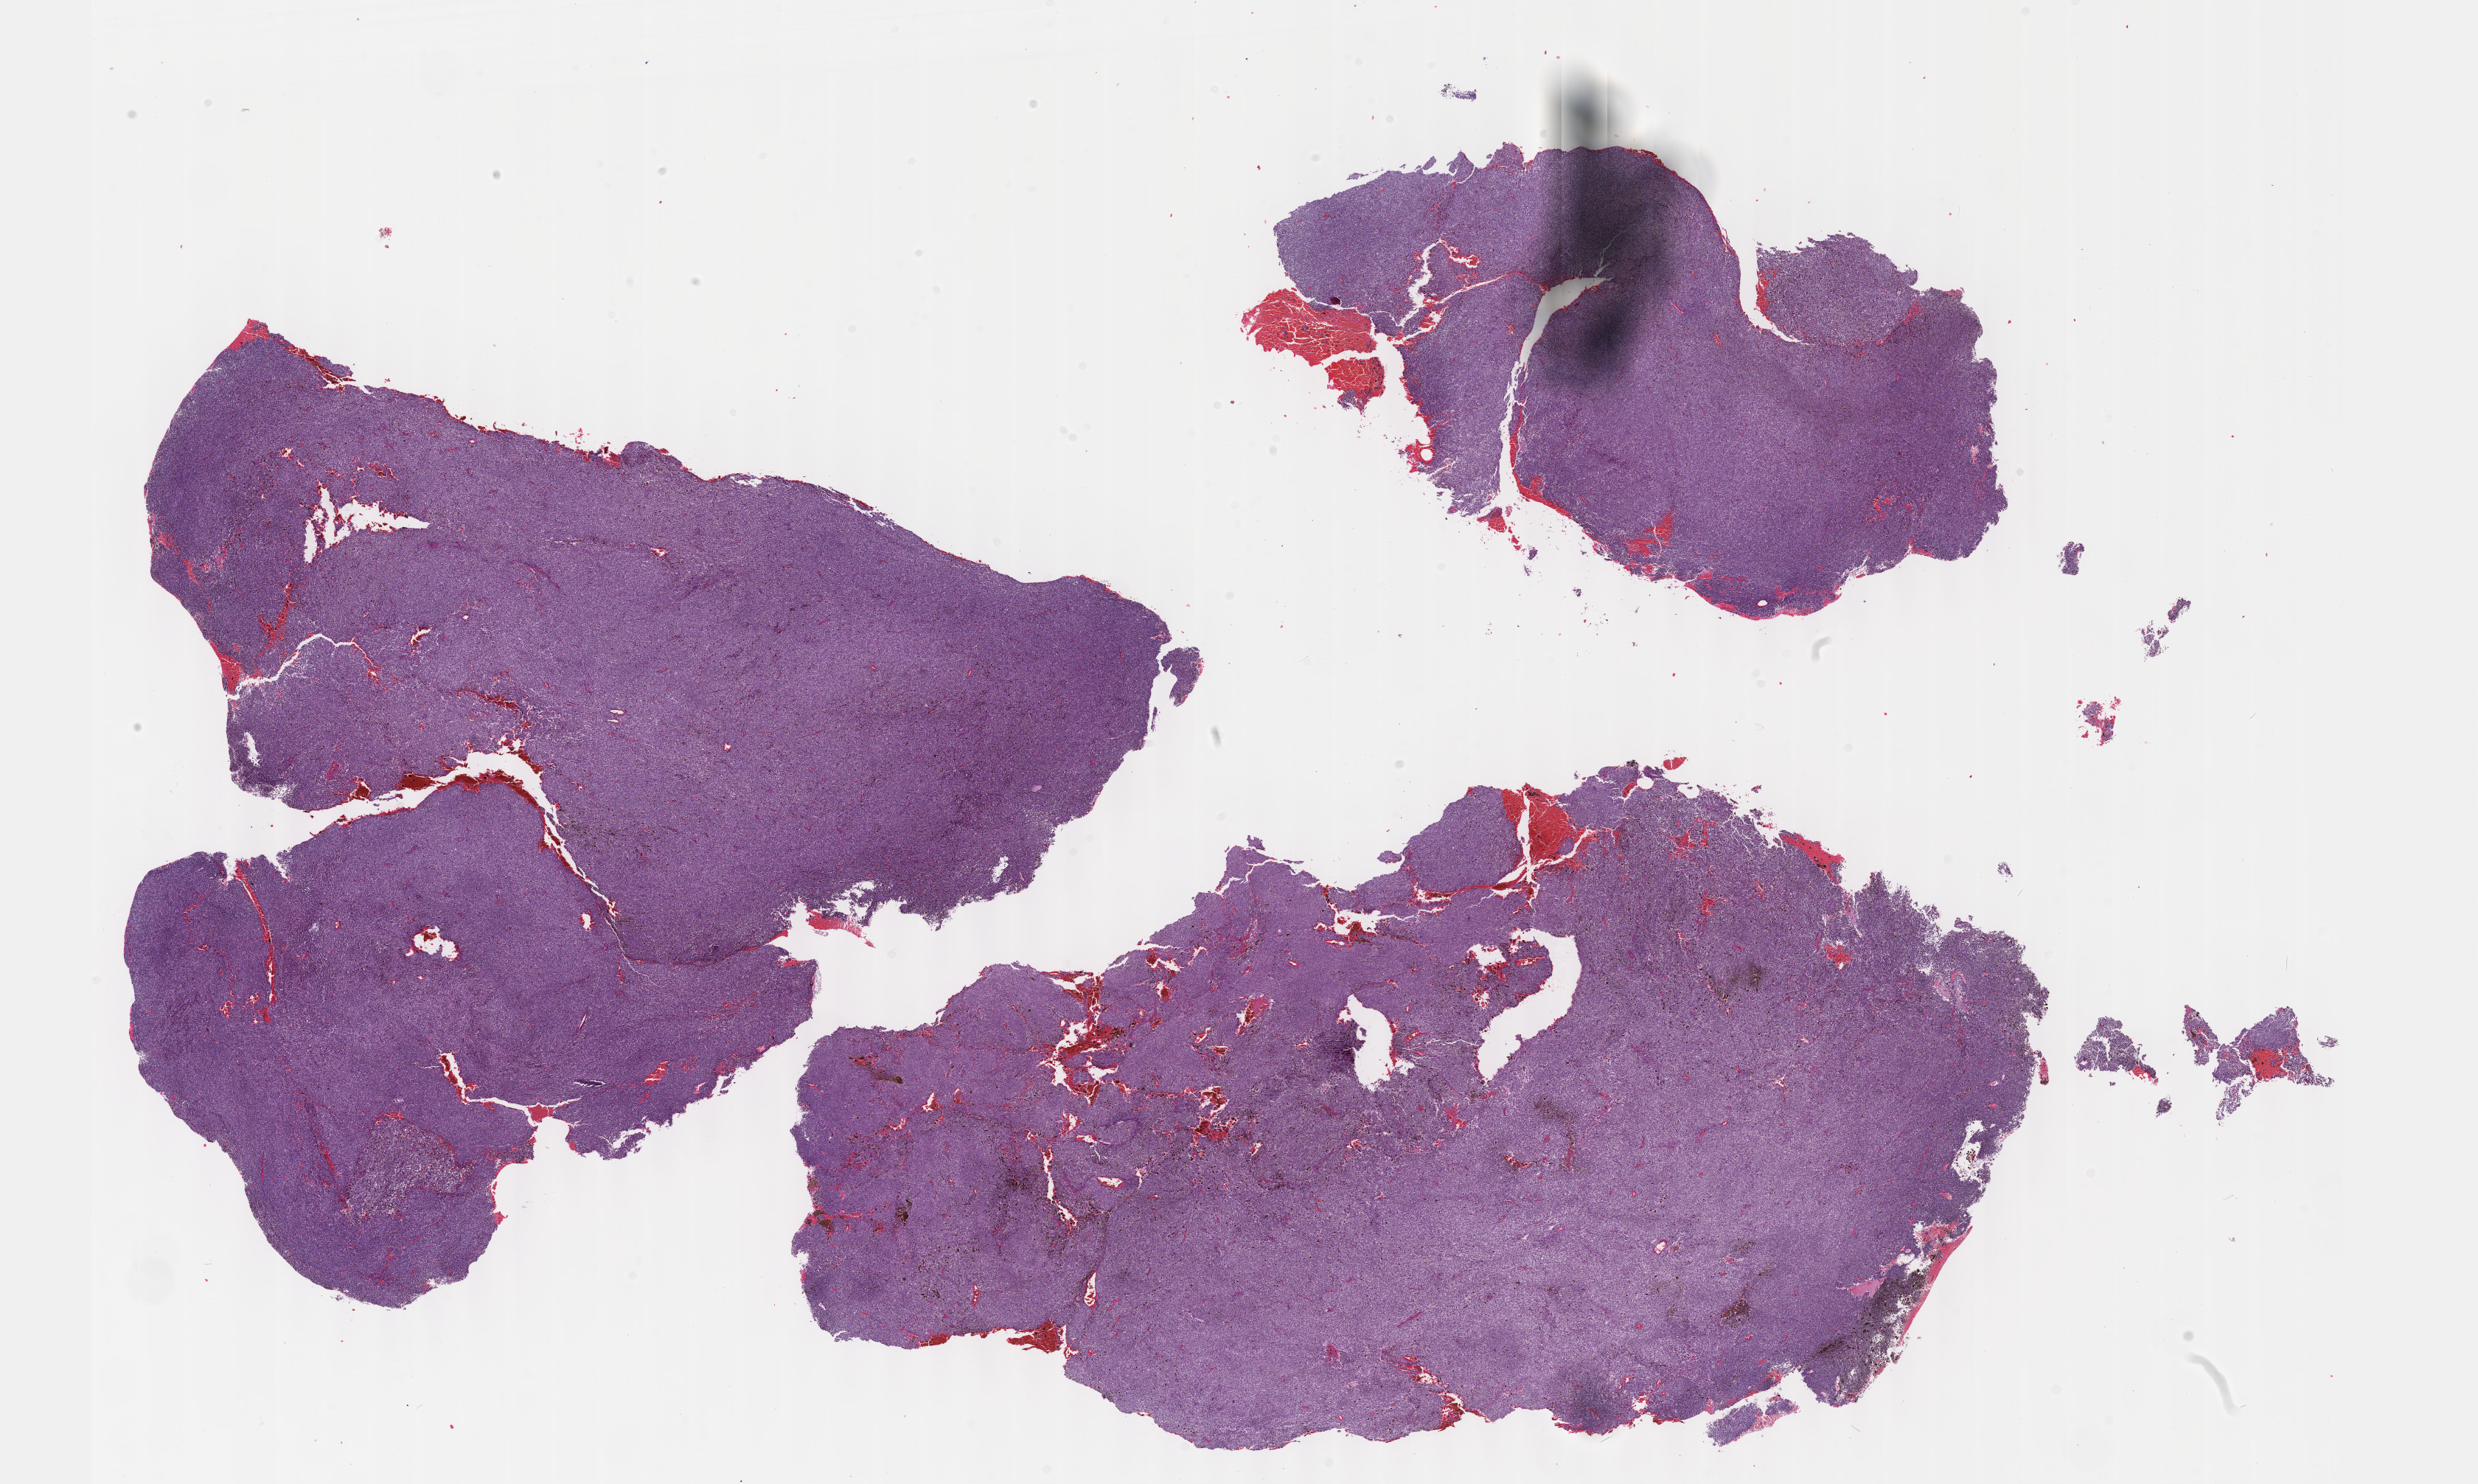
H&E-stained whole-slide image — low-resolution overview of the scanned area, about 27.2 x 16.3 mm (slide scanned at 40x); FFPE section; uvea, primary tumour sample. Male, age 60 years at initial diagnosis.
Histologic diagnosis: Spindle cell melanoma, type B (choroid).